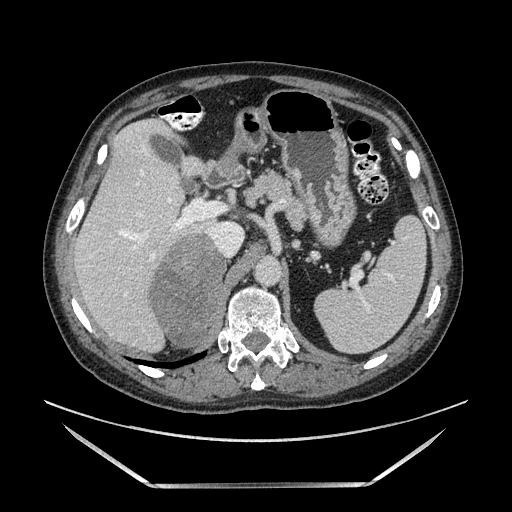
Contrast-enhanced abdominal CT, one axial slice; position 95 of 185 along the scan axis; soft-tissue window (W 400 / L 40 HU); 1.25 mm slice thickness; 512 × 512 image matrix, field of view 440 × 440 mm. Male patient. From the clinical record (not read from this slice): diagnosis: adrenocortical carcinoma; tumour side: right adrenal; tumour size at pathology: 10.3 cm; Ki-67 index: 20 %; stage (as recorded): 3.
Annotated regions visible in this slice (semi-automatic segmentation, software-assisted and operator-edited):
- mass: bounding box <151,230,226,348> (left, top, right, bottom; pixels)